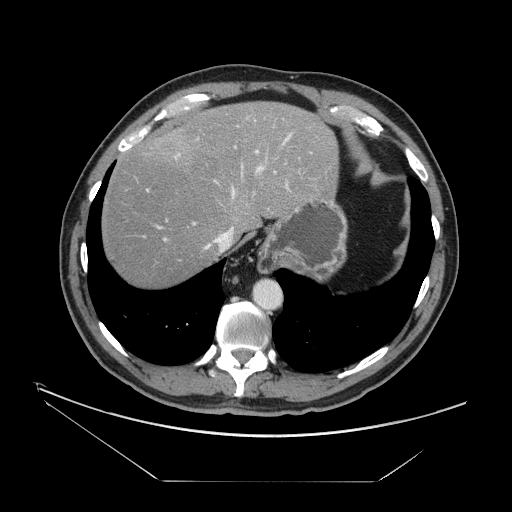
Contrast-enhanced abdominal CT, one axial slice. Reconstruction kernel STANDARD. 120 kVp. Intravenous contrast given. Soft-tissue window (W 400 / L 40 HU). 2.5 mm slice thickness. 512 × 512 image matrix. Male patient, age 65 years. Case-level facts recorded for this patient, not image findings: diagnosis: colorectal cancer liver metastases, imaged before liver resection; multiple liver metastases: yes; largest metastasis: 4.2 cm; disease in both lobes: yes.
Structures marked on this image (manually delineated by an expert):
- hepatic veins: bounding box <203,126,291,253> (left, top, right, bottom; pixels)
- liver: <101,102,337,287>
- planned liver remnant (the part of the liver to remain after resection): <101,102,337,287>
- portal vein (with intrahepatic branches): <146,116,312,241>